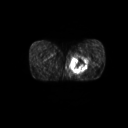
FDG PET of an extremity soft-tissue mass (from a PET/CT study), one axial slice; position 22 of 267 along the scan axis; 128 × 128 image matrix, field of view 600 × 600 mm. Patient: male, 59 years. From the clinical record (not read from this slice): histological type: pleiomorphic liposarcoma; grade: high; site of the primary tumour: left thigh.
Structures marked on this image (expert contour drawn on MRI and transferred to this co-registered scan by the dataset authors):
- gross tumour volume including surrounding oedema: bounding box (x1, y1, x2, y2) in pixels: (71, 54, 91, 75)
- gross tumour volume (mass): (71, 56, 88, 73)